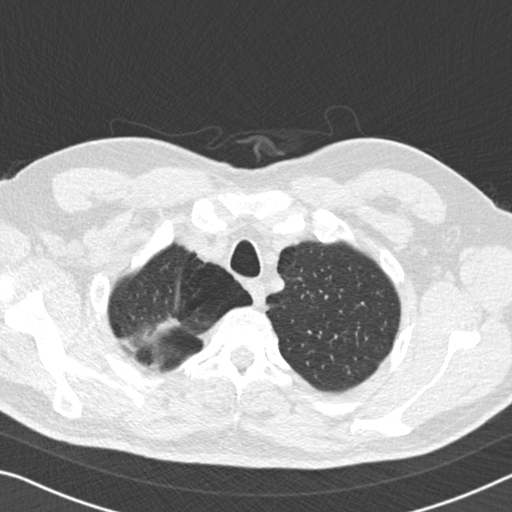
Low-dose screening chest CT, one axial slice; position 146 of 167 along the scan axis; reconstruction kernel B30f; lung window (W 1500 / L -600 HU); 2 mm slice thickness; 512 × 512 image matrix.
Outlined on this slice (manually delineated by an expert):
- lesion 1 (tumor, upper lobe of right lung): bounding box [x1, y1, x2, y2] px = [133, 318, 180, 350]